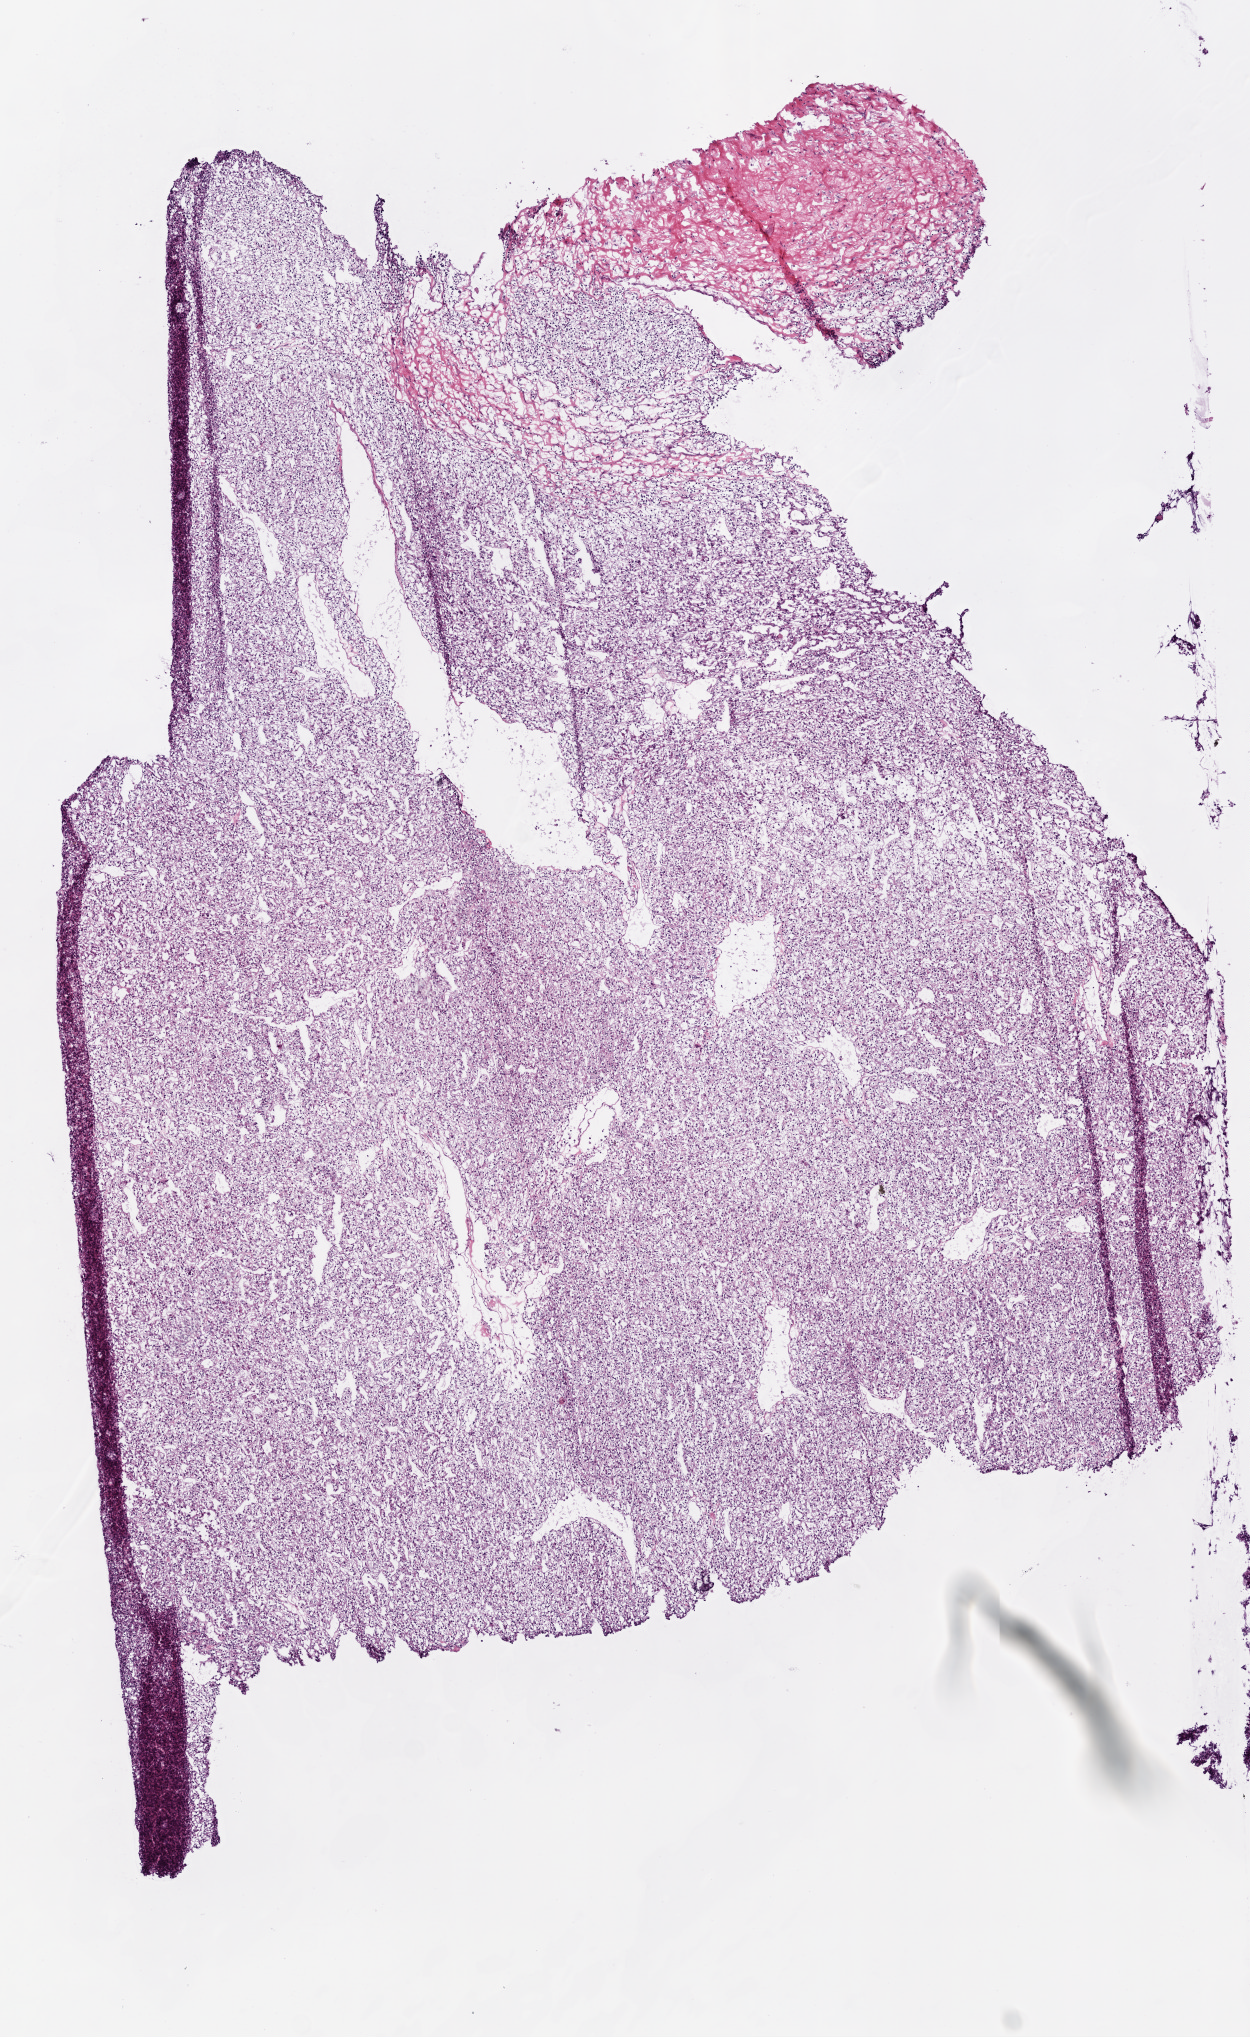
H&E whole-slide image — shown as a low-resolution overview of the whole scanned area (about 5.0 x 8.2 mm); frozen section from the top of the tissue portion; kidney, primary tumour sample. Female, age 51 years at initial diagnosis. Histologic grade: G2 (moderately differentiated). Slide review estimates, as recorded: tumour cells 90%, tumour nuclei 90%, normal cells 0%, stromal cells 10%, necrosis 0%.
AJCC pathologic stage: III (6th edition). Pathologic diagnosis: Clear cell adenocarcinoma, NOS.